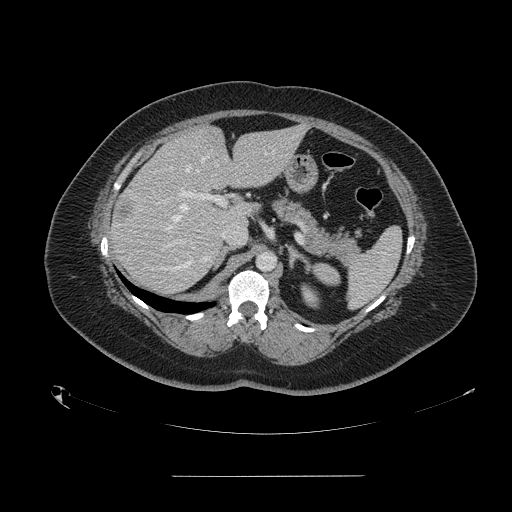
Contrast-enhanced abdominal CT, one axial slice; slice 95 of 164 in the series (ordered by position); 120 kVp; soft-tissue window (W 400 / L 40 HU); 512 × 512 image matrix, field of view 495 × 495 mm. Female patient, age 52 years. From the clinical record (not read from this slice): diagnosis: colorectal cancer liver metastases, imaged before liver resection; multiple liver metastases: yes; largest metastasis: 3.5 cm; disease in both lobes: no.
Annotated regions visible in this slice (expert manual segmentation):
- hepatic veins: box from (x=165, y=151) to (x=274, y=230) px
- liver: (x=111, y=126)–(x=304, y=293)
- planned liver remnant (the part of the liver to remain after resection): (x=175, y=126)–(x=303, y=227)
- portal vein (with intrahepatic branches): (x=158, y=168)–(x=227, y=246)
- liver metastasis: (x=190, y=259)–(x=203, y=274)
- liver metastasis: (x=117, y=202)–(x=132, y=226)